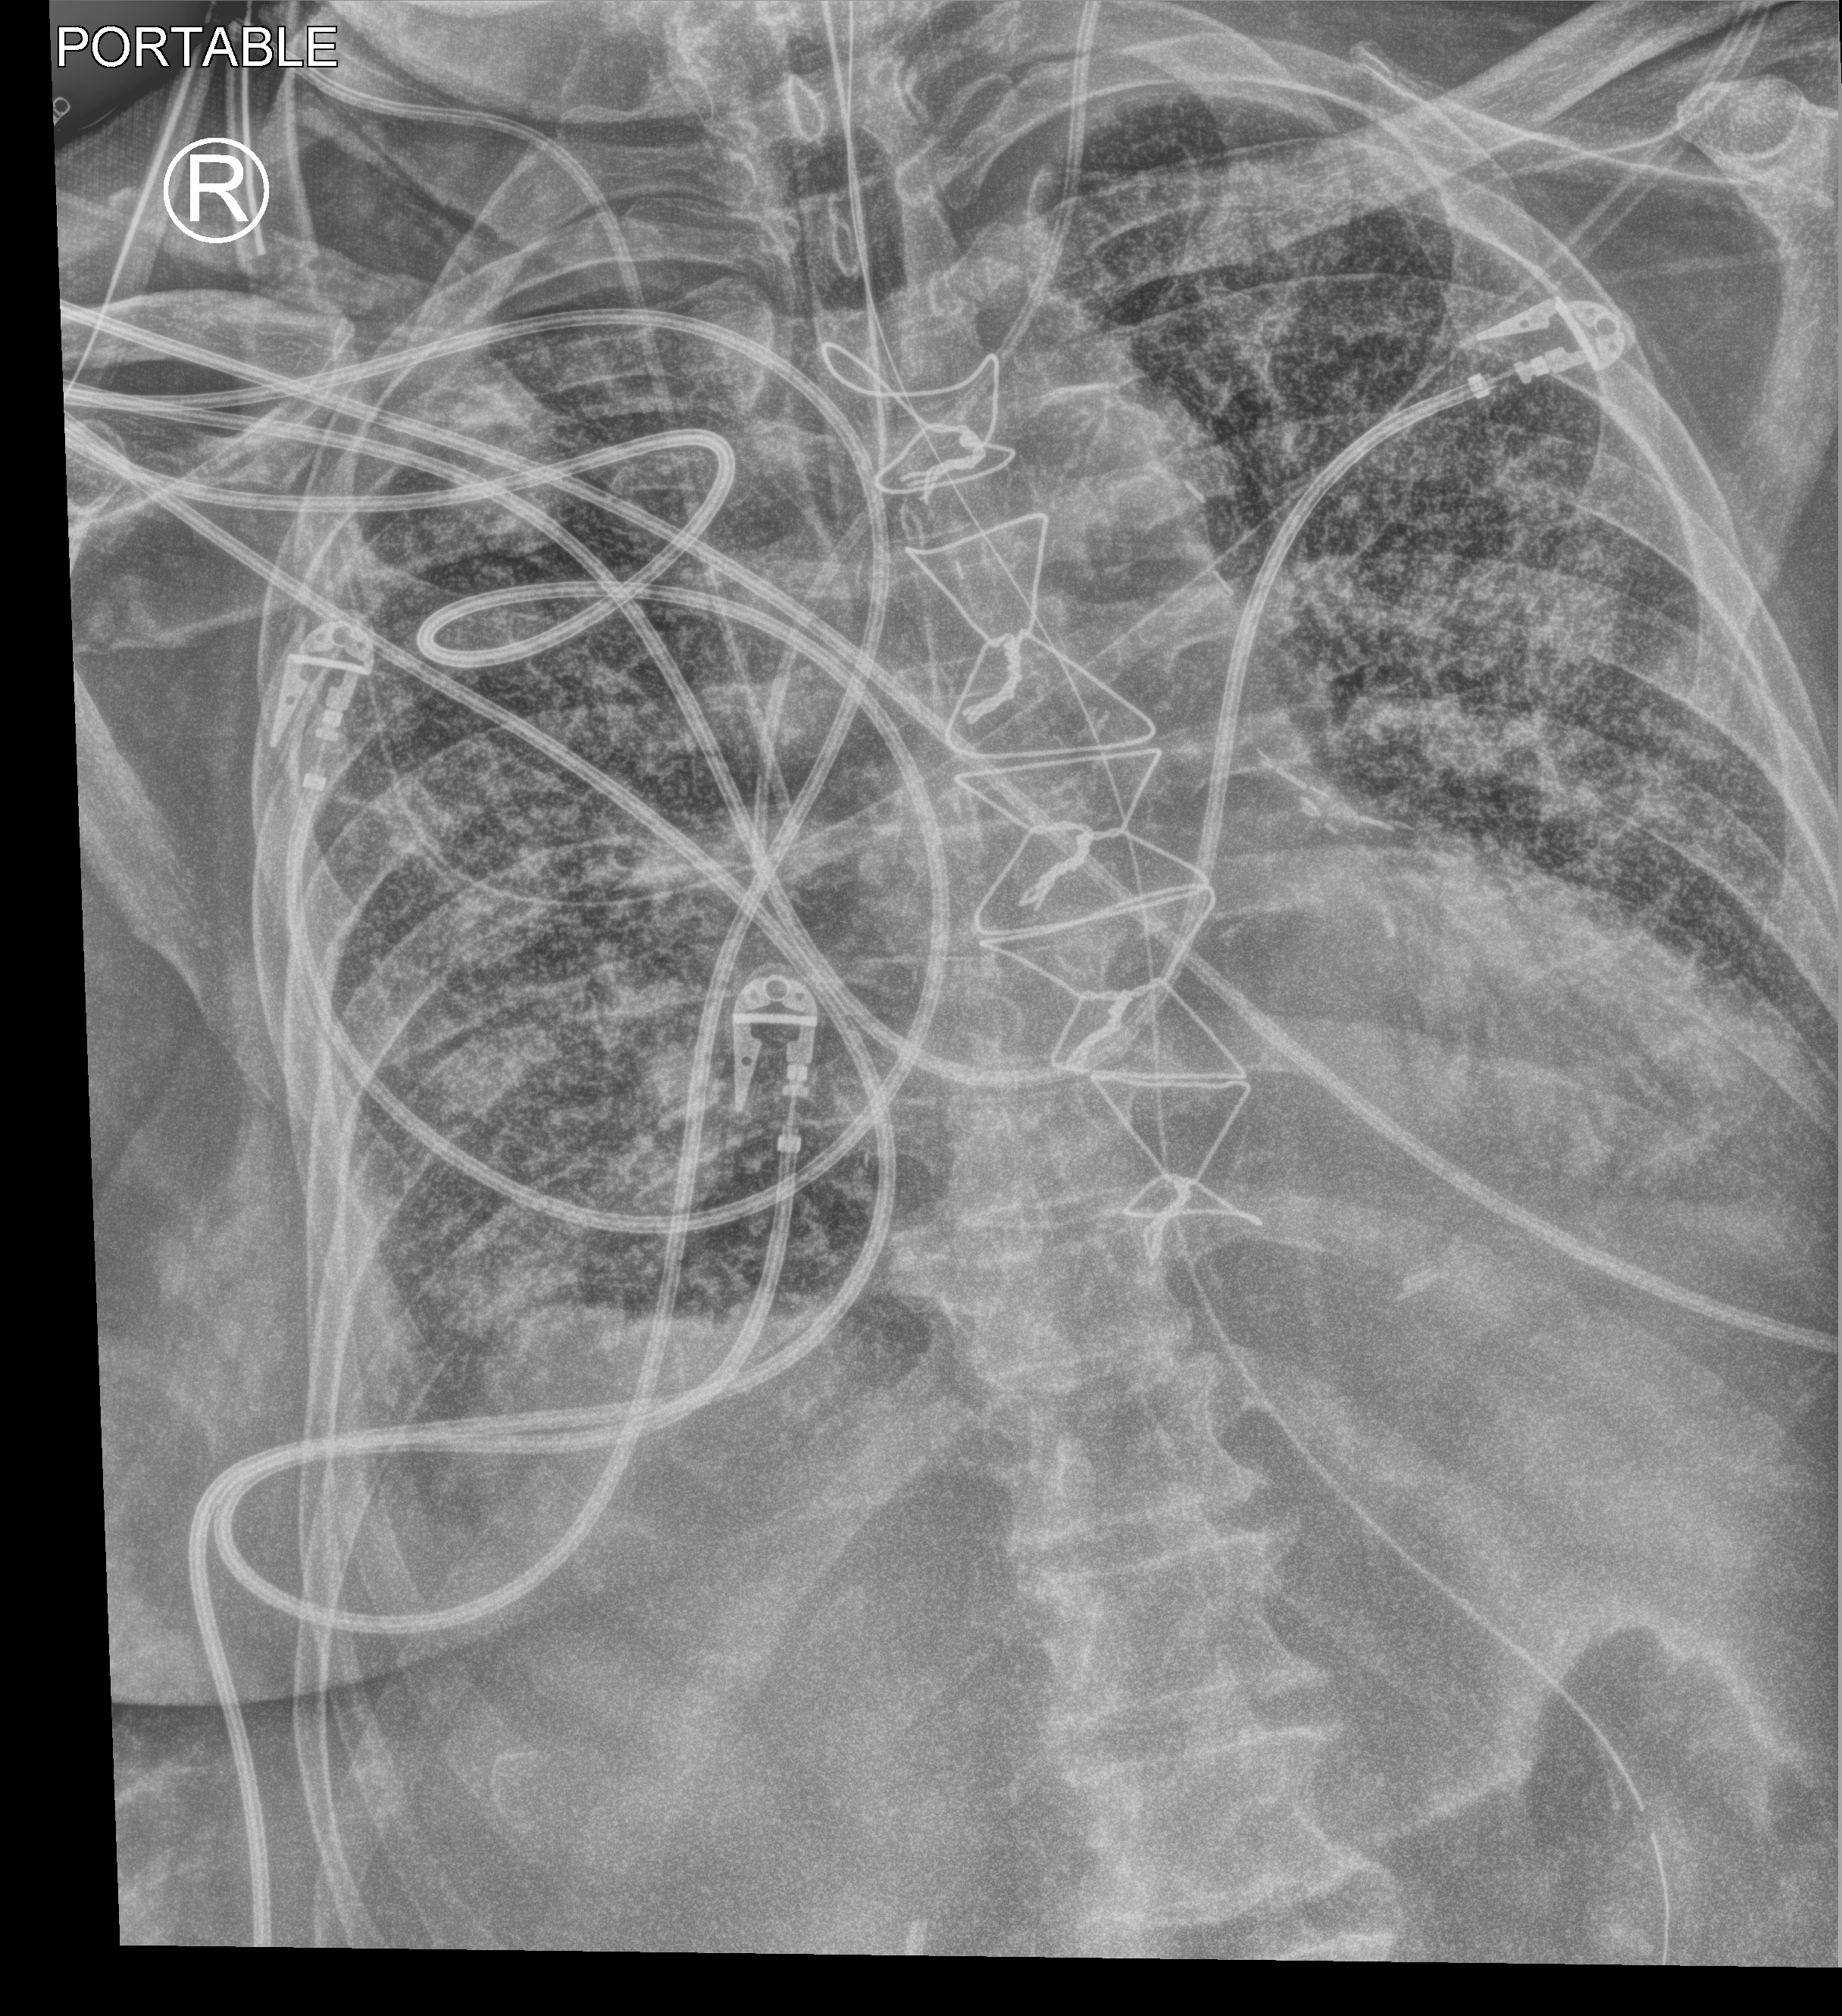
Chest X-ray (portable). Male patient hospitalised with COVID-19, age 75–90 years.
Admission-level facts for this patient (not findings on this image; timing relative to this image not recorded): COPD (admission record): yes.